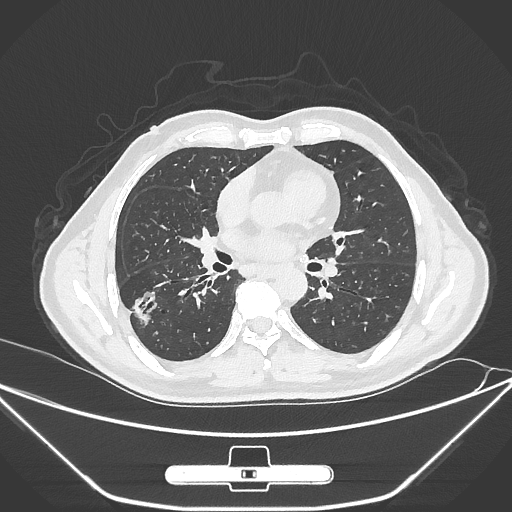
Chest CT, one axial slice. Position 147 of 310 along the scan axis. Lung window (W 1500 / L -600 HU). 1 mm slice thickness. 512 × 512 image matrix, field of view 398 × 398 mm. Patient: male, 71 years. Case-level facts recorded for this patient, not image findings: clinical TNM (as recorded): T1c N0 M0; histopathological grade: G2.
Annotated regions visible in this slice (bounding box drawn by a radiologist):
- lung tumour (recorded histology: adenocarcinoma): box from (x=121, y=284) to (x=164, y=333) px